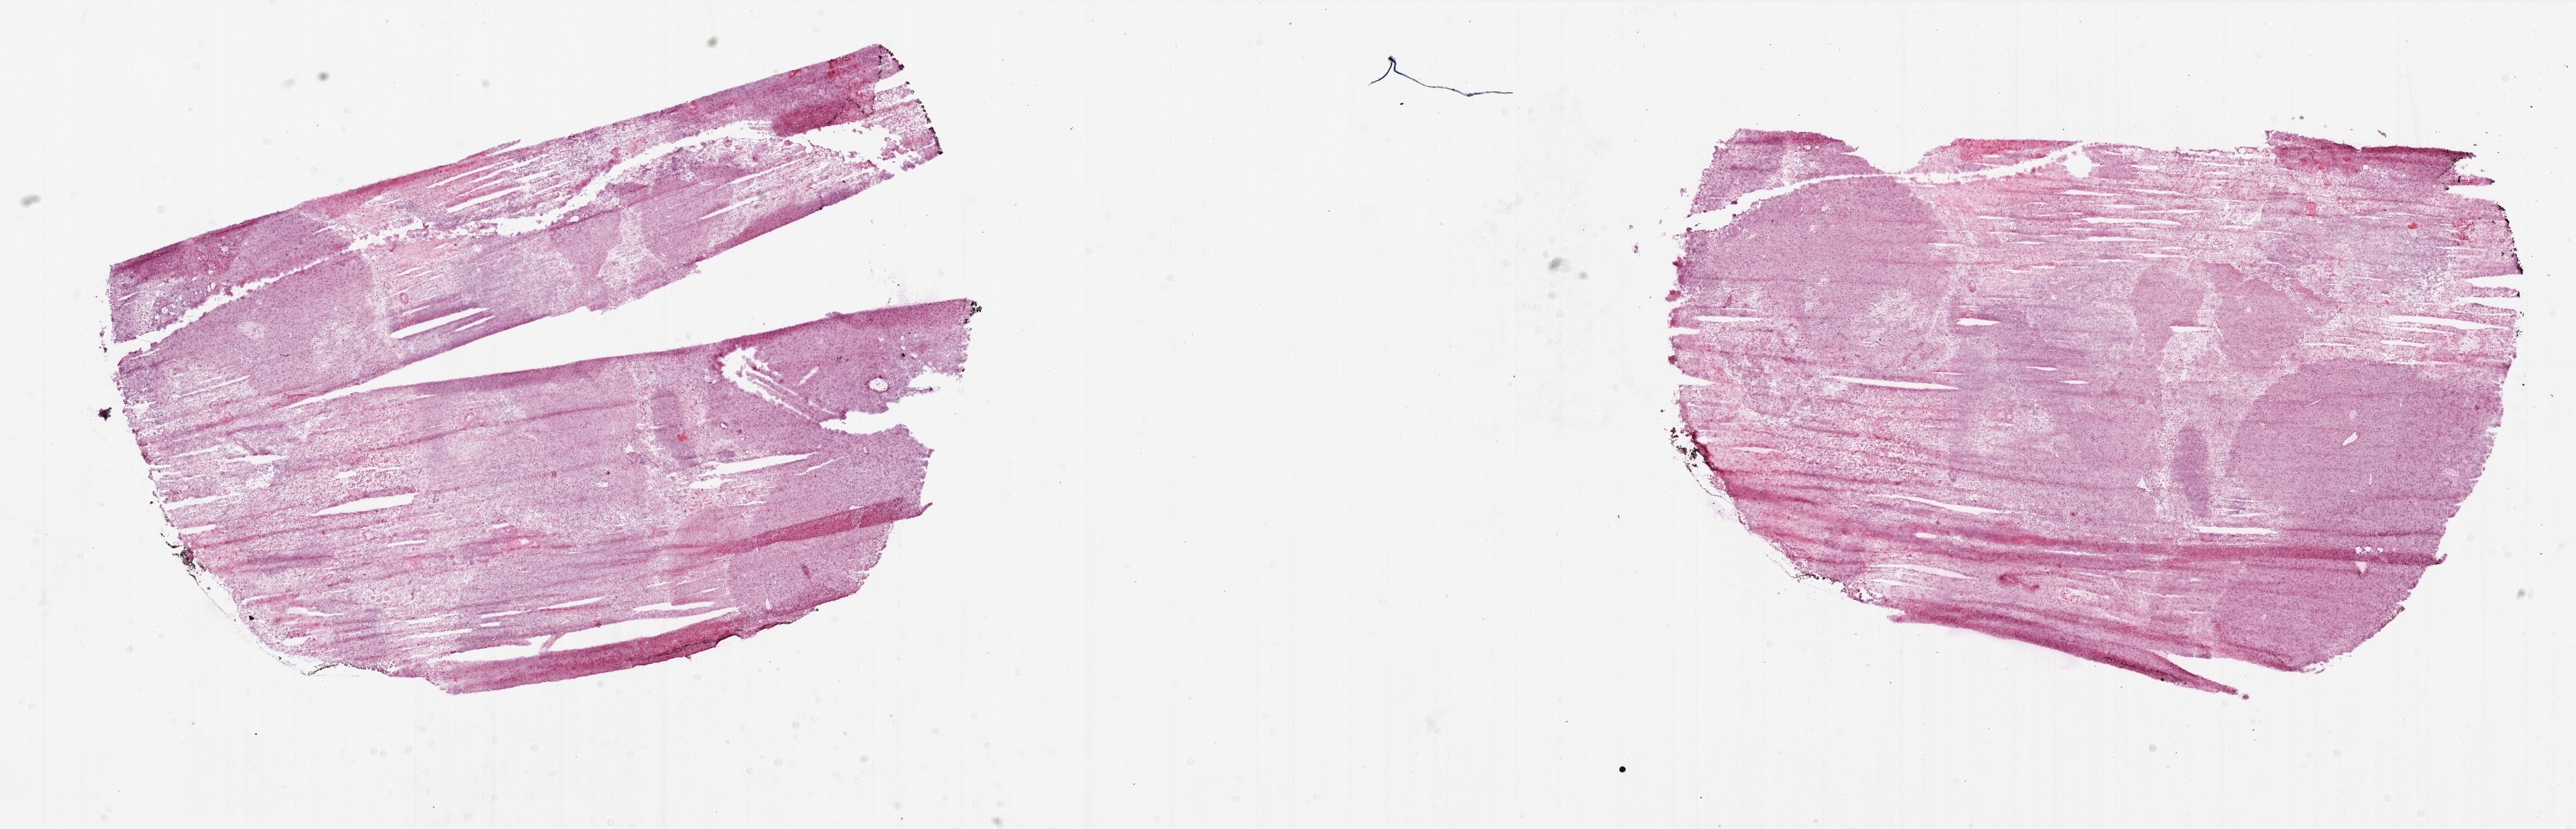
Hematoxylin and eosin (H&E) stained whole-slide image — low-resolution overview of the scanned area, about 30.0 x 9.6 mm (slide scanned at 20x); frozen section from the bottom of the tissue portion; brain, primary tumour sample. Male patient; age at initial diagnosis 62 years. Pathologist review of this section (percent, as recorded): tumour cells 60%, tumour nuclei 100%, normal cells 0%, stromal cells 0%, necrosis 40%. Inflammatory infiltration, as recorded: lymphocyte infiltration 0%, monocyte infiltration 0%, neutrophil infiltration 0%.
Pathologic diagnosis: Glioblastoma.